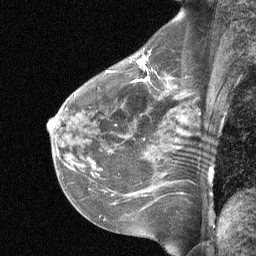
Breast MRI (dynamic contrast-enhanced), one sagittal slice. Position 39 of 64 along the scan axis. Dynamic contrast-enhanced study with each time point stored as its own series, time point 2 of 3 at this slice position (early post-contrast, ordered by acquisition time). 1.5 T. TE 4.8 ms, TR 27 ms. 2 mm slice thickness. 256 × 256 image matrix, field of view 200 × 200 mm. Patient: female, 51 years. From the clinical record (not read from this slice): setting: breast cancer imaged before/during neoadjuvant chemotherapy; receptor status: HR-positive, HER2-negative.
Outlined on this slice (semi-automatically segmented with operator editing):
- analysis volume of interest (the breast-tissue region the enhancement analysis was run in; not a lesion): box from (x=88, y=42) to (x=196, y=119) px
- tumour enhancement mask (voxels above the 90 % enhancement threshold inside the analysis volume of interest): (x=133, y=58)–(x=149, y=83)